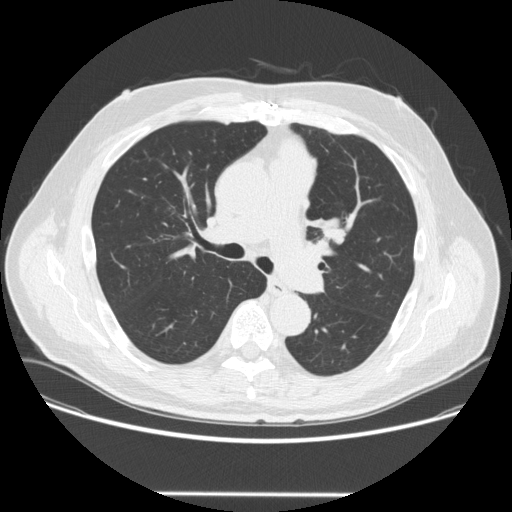
Chest CT (low-dose screening protocol), one axial image; third annual screen; lung window (W 1500 / L -600 HU); 120 kVp; slice 90 of 253 in the series; 512 × 512 image matrix. Male participant, aged 66 years at enrolment. Former smoker at enrolment.
- Expert reader's lesion annotation, box from (x=309, y=205) to (x=361, y=254) px.
- The screening reader recorded 2 non-calcified nodules or masses ≥4 mm on this exam (left upper lobe, right lower lobe); which of them this box marks is not recorded.
- Participant outcome: lung cancer diagnosed 85 days after this screen — squamous cell carcinoma, NOS, left upper lobe, poorly differentiated (G3), stage IA (AJCC 6th edition), 27 mm at pathology.